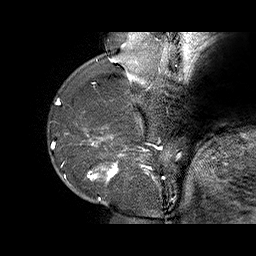
Breast MRI (dynamic contrast-enhanced), one sagittal slice. Slice 15 of 70 in the series (ordered by position). Dynamic contrast-enhanced series, time point 2 of 6 at this slice position (early post-contrast). 1.5 T. TE 4.5 ms, TR 32.4 ms. 3 mm slice thickness. 256 × 256 image matrix. Female patient. Case-level facts recorded for this patient, not image findings: setting: breast cancer imaged before/during neoadjuvant chemotherapy; receptor status: HR-positive, HER2-negative.
Annotated regions visible in this slice (semi-automatic segmentation, software-assisted and operator-edited):
- analysis volume of interest (the breast-tissue region the enhancement analysis was run in; not a lesion): bounding box <71,128,159,202> (left, top, right, bottom; pixels)
- tumour enhancement mask (voxels above the 100 % enhancement threshold inside the analysis volume of interest): <87,136,156,200>